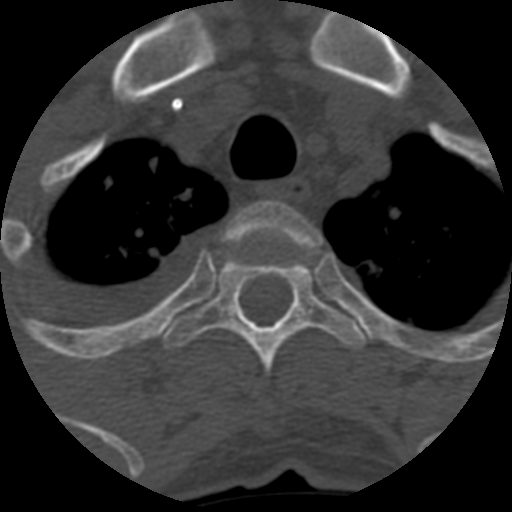
CT including the spine, one axial slice. Position 492 of 708 along the scan axis. Reconstruction kernel STANDARD. 120 kVp. One of 3 acquisitions stored at this slice position. Bone window (W 1800 / L 400 HU). 1.25 mm slice thickness. 512 × 512 image matrix. Patient age 55 years. Case-level facts recorded for this patient, not image findings: primary cancer: colon; vertebrae with lytic lesions (as recorded): T12, L1, L5.
Outlined on this slice (semi-automatically segmented with operator editing):
- T2 vertebra: bounding box <226,201,320,247> (left, top, right, bottom; pixels)
- T3 vertebra: <161,250,365,376>